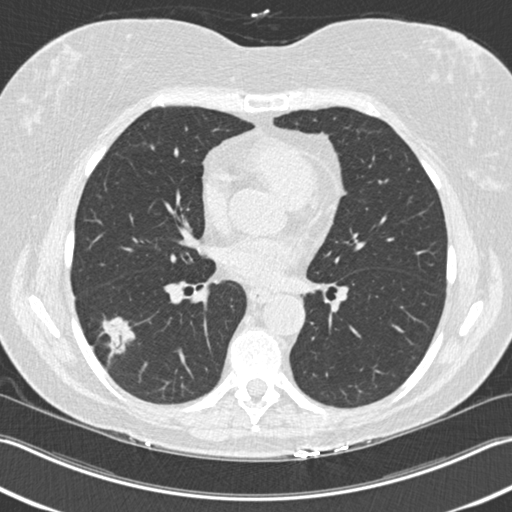
Low-dose screening chest CT, axial slice, first (baseline) screen, lung window (W 1500 / L -600 HU), slice 97 of 211 in the series, 512 × 512 image matrix, field of view 348 × 348 mm. Female, age 63 years at enrolment. Current smoker at enrolment.
- Expert-annotated lung lesion, bounding box <76,313,139,370> (left, top, right, bottom; pixels).
- The screening reader recorded 3 non-calcified nodules or masses ≥4 mm on this exam (right upper lobe, right lower lobe, right lower lobe); which of them this box marks is not recorded.
- Participant outcome: lung cancer diagnosed 57 days after this screen — bronchiolo-alveolar adenocarcinoma, NOS, right lower lobe, well differentiated (G1), stage IA (AJCC 6th edition), 25 mm at pathology.